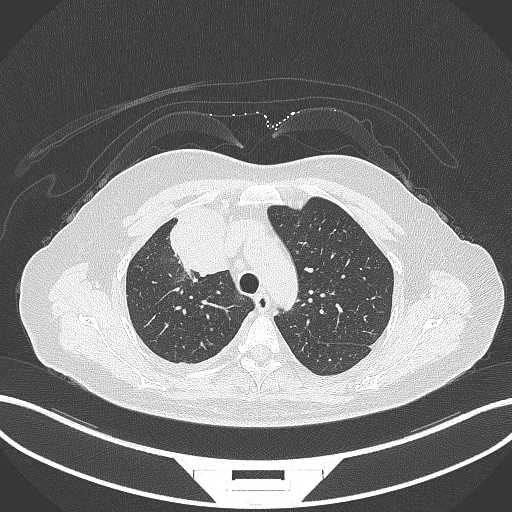
Chest CT, one axial slice; position 224 of 305 along the scan axis; lung window (W 1500 / L -600 HU); 1 mm slice thickness; 512 × 512 image matrix, field of view 400 × 400 mm. Female patient, age 52 years. Case-level facts recorded for this patient, not image findings: clinical TNM (as recorded): T3 N1 M1.
Structures marked on this image (bounding box drawn by a radiologist):
- lung tumour (recorded histology: adenocarcinoma): bounding box (x1, y1, x2, y2) in pixels: (165, 204, 237, 277)